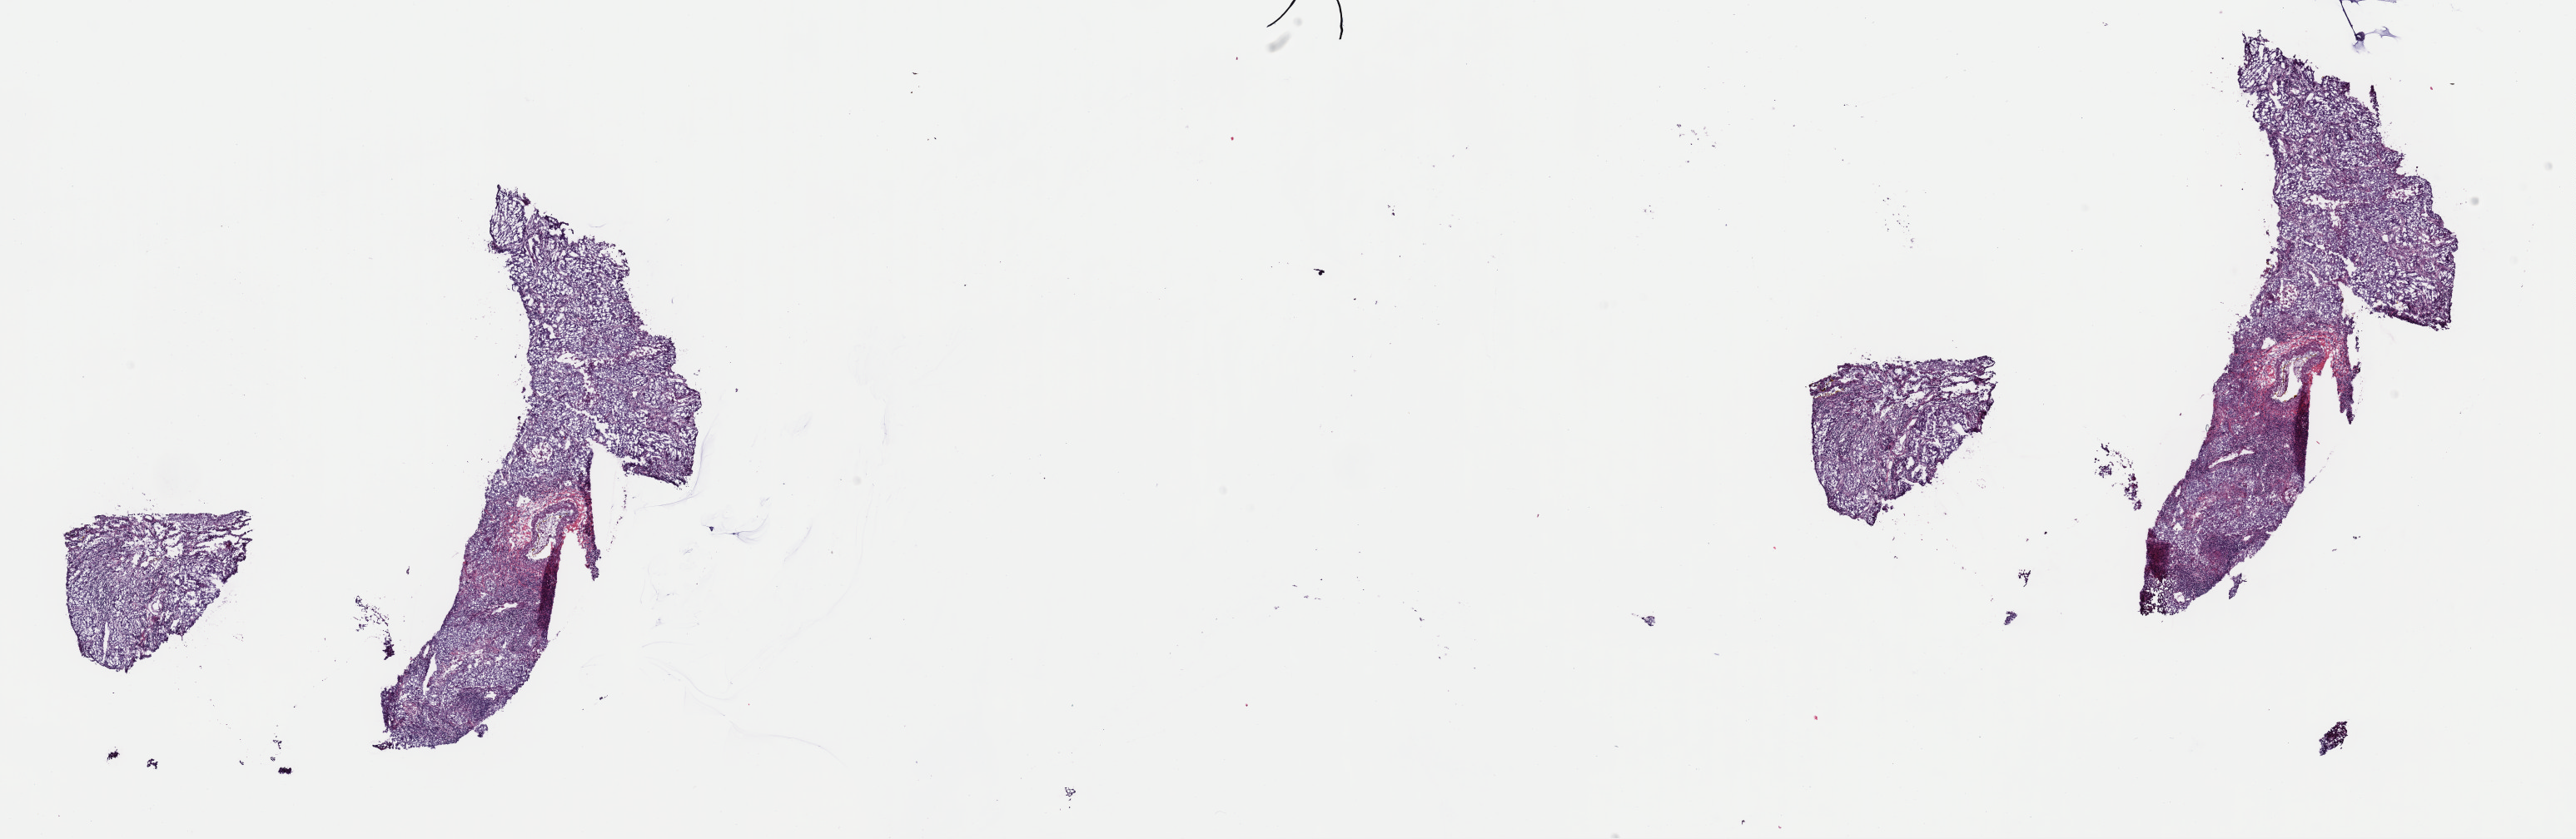
H&E-stained whole-slide image — whole scanned area (about 24.4 x 8.0 mm, from a 40x scan) shown as a low-resolution overview; frozen section from the top of the tissue portion; lung, primary tumour sample. Patient: female, age at initial diagnosis 54 years. Pathologist review of this section (percent, as recorded): tumour cells 82%, tumour nuclei 90%, normal cells 0%, stromal cells 15%, necrosis 3%. Inflammatory infiltration, as recorded: lymphocyte infiltration 10%, monocyte infiltration 1%, neutrophil infiltration 2%.
Histologic diagnosis: Adenocarcinoma, NOS (upper lobe, lung). AJCC pathologic stage: IB.